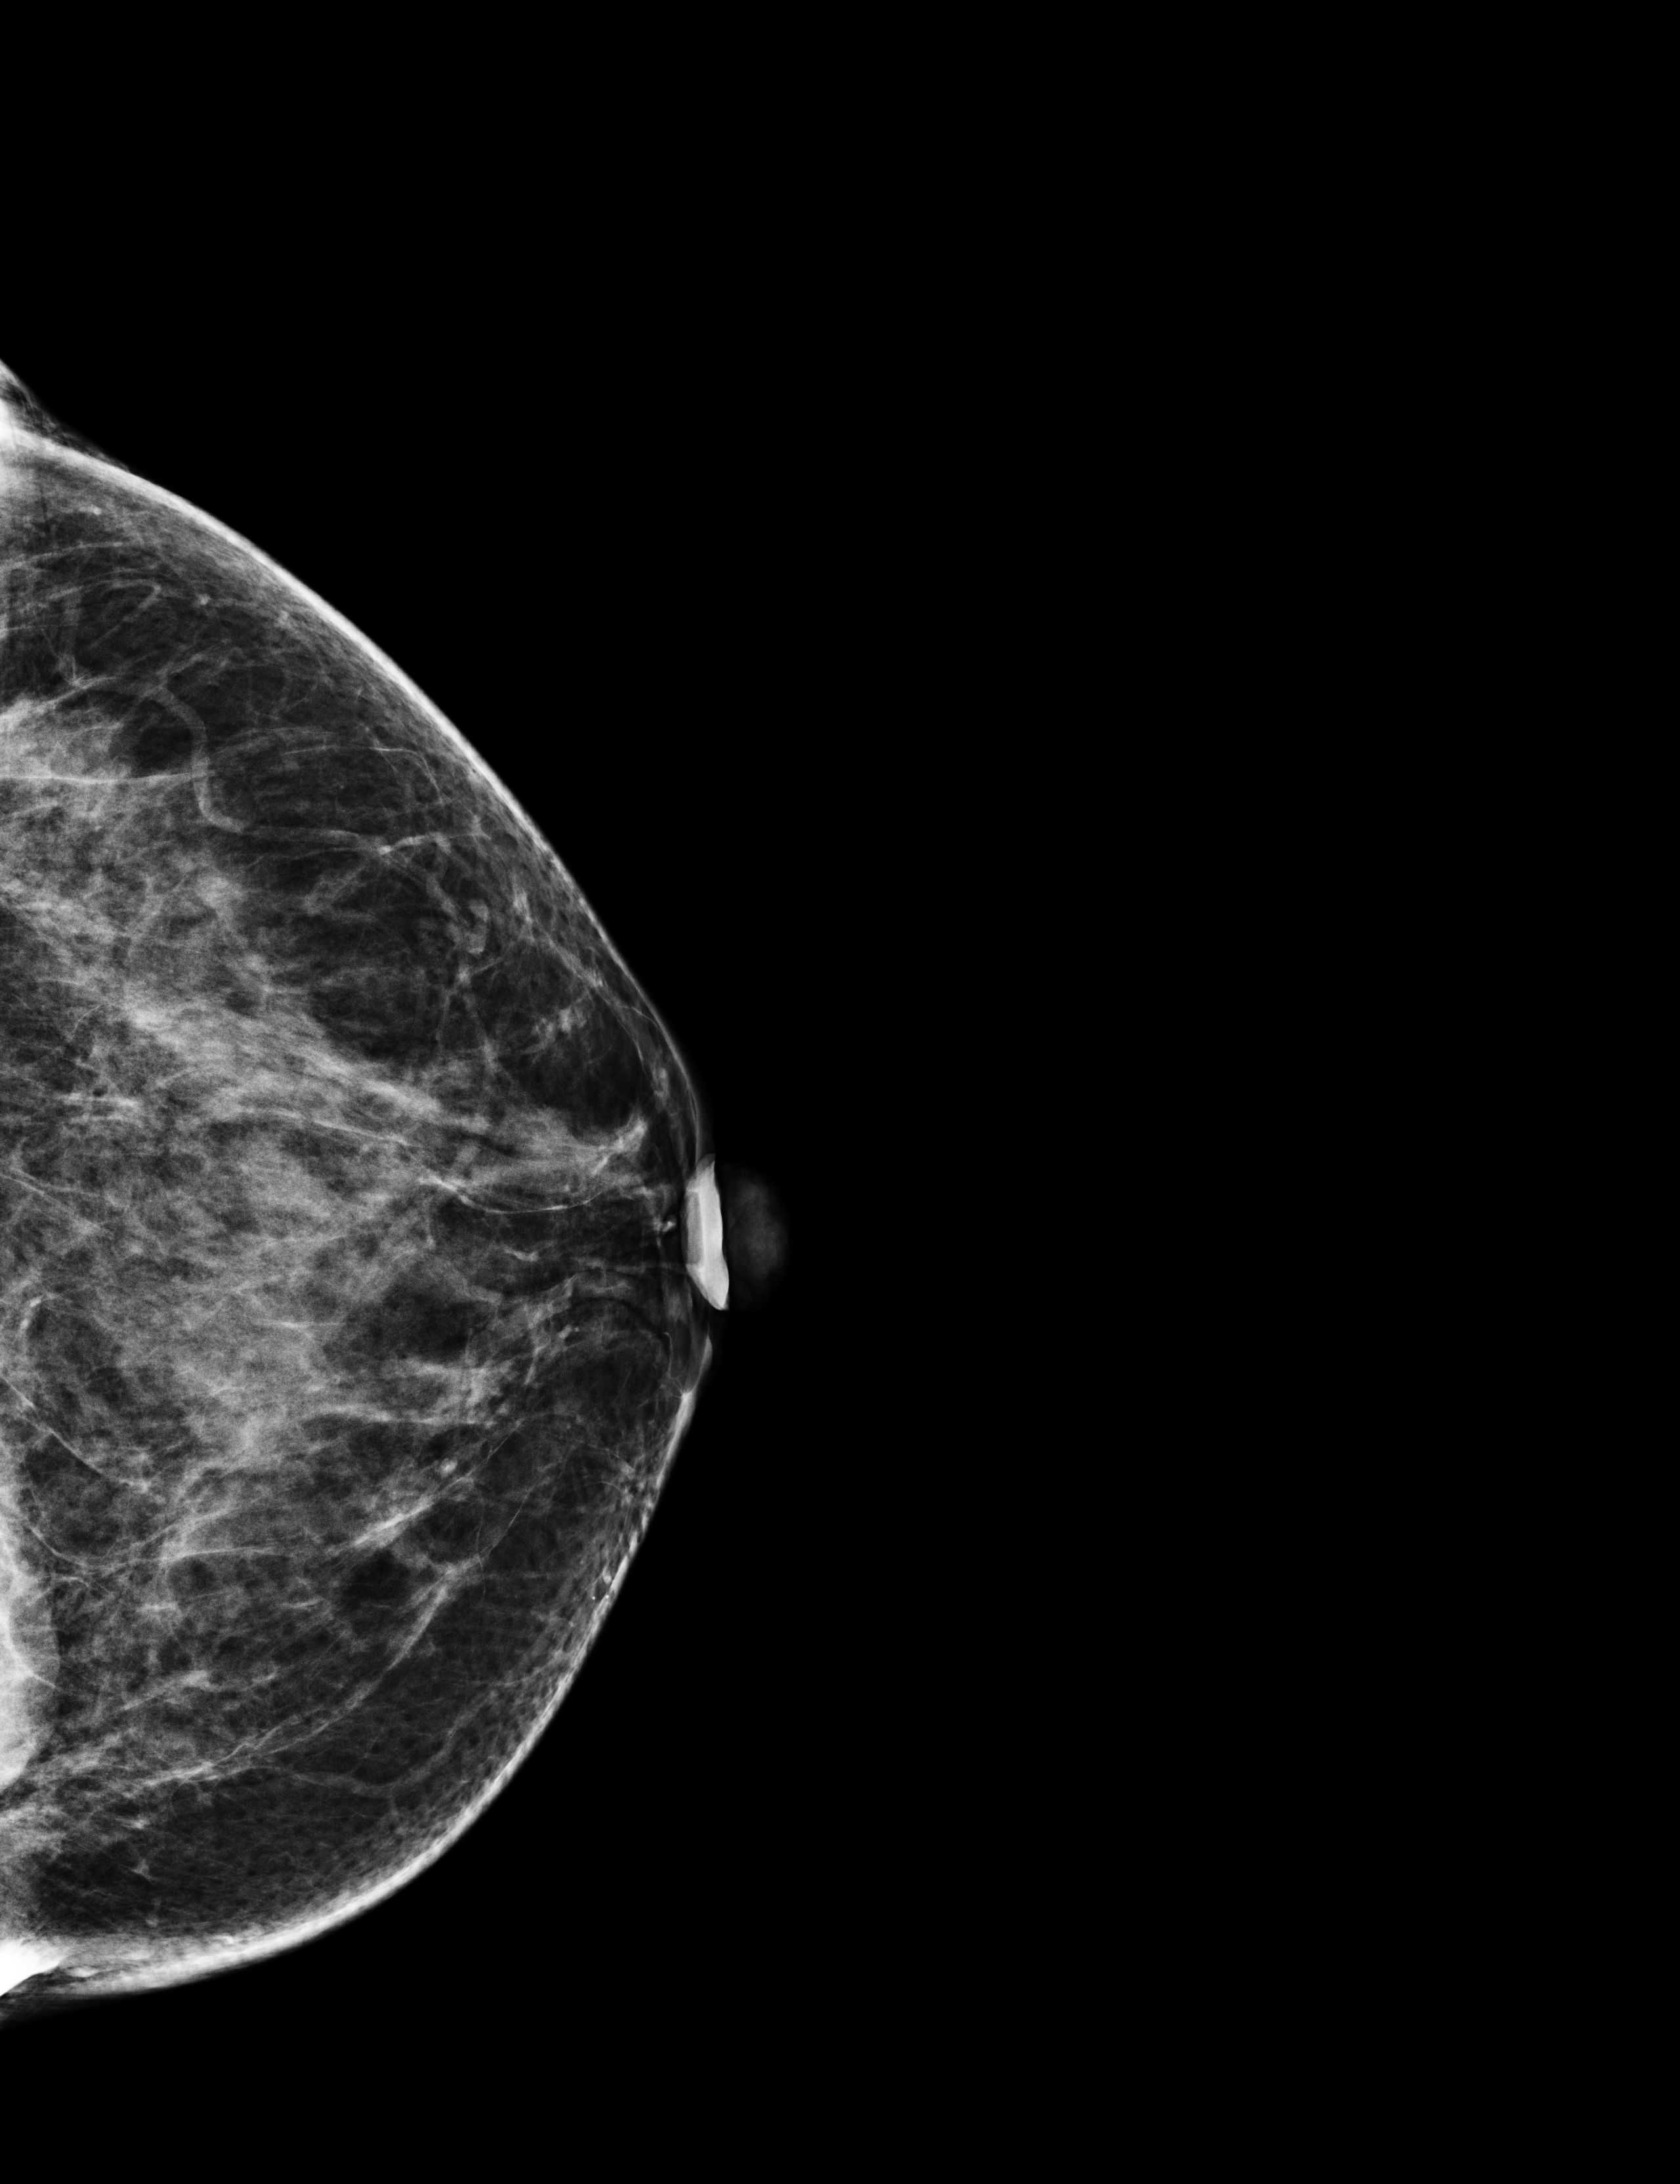
Annual screening mammography examination, compressed breast thickness 57 mm, system: Selenia Dimensions. Patient: female, 62 years.
Image type: full-field digital mammogram. Breast: left. Projection: craniocaudal (CC) view.